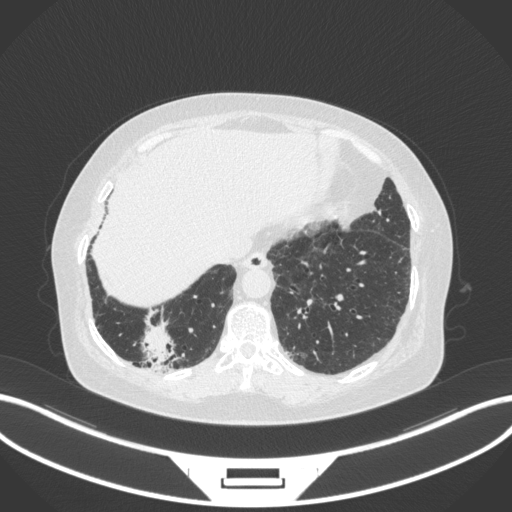
Chest CT, one axial slice. Position 31 of 303 along the scan axis. 120 kVp. Lung window (W 1500 / L -600 HU). 1 mm slice thickness. 512 × 512 image matrix, field of view 400 × 400 mm. Female patient, age 65 years. From the clinical record (not read from this slice): clinical TNM (as recorded): T2b N1 M0; histopathological grade: G1.
Outlined on this slice (rectangle marked by the reading radiologist):
- lung tumour (recorded histology: adenocarcinoma): box from (x=134, y=321) to (x=180, y=367) px